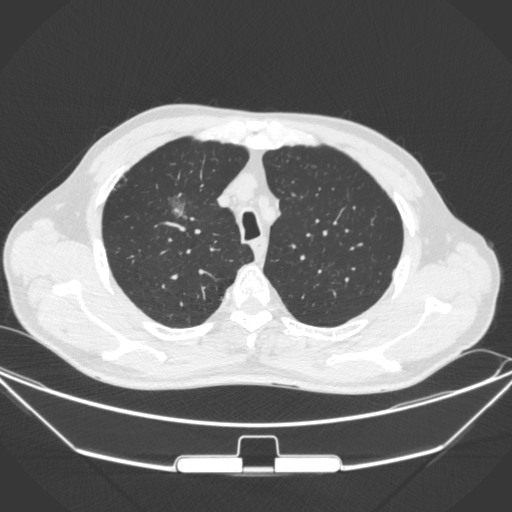
Chest CT, one axial slice; position 270 of 355 along the scan axis; lung window (W 1500 / L -600 HU); 1 mm slice thickness; 512 × 512 image matrix. Male patient, age 67 years. From the clinical record (not read from this slice): clinical TNM (as recorded): T1c N0 M0.
Outlined on this slice (rectangle marked by the reading radiologist):
- lung tumour (recorded histology: adenocarcinoma): bounding box <158,190,207,236> (left, top, right, bottom; pixels)